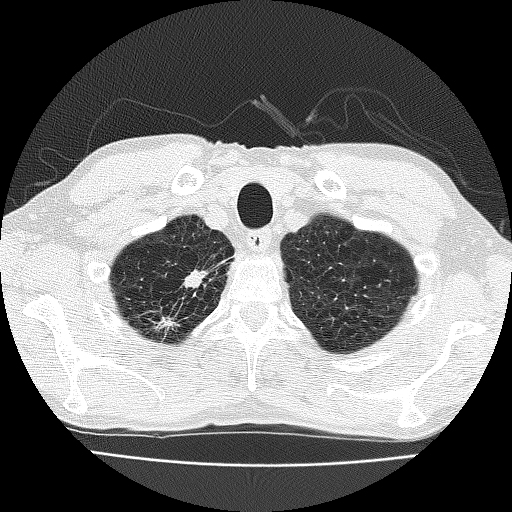
Chest CT (low-dose screening protocol), one axial image. Third screening round (two years after baseline). Lung window (W 1500 / L -600 HU). Lung (sharp) reconstruction kernel (FC51). Male, age 63 years at enrolment. Current smoker at enrolment.
Expert-annotated lung lesion, bounding box [x1, y1, x2, y2] px = [144, 257, 224, 336]. Reader record for this screening exam (exam-level; its link to the box is not recorded): non-calcified nodule or mass ≥4 mm, right upper lobe, 17 × 10 mm, spiculated (stellate) margins, soft tissue attenuation, pre-existing on the prior screen: yes; interval growth: yes. Later outcome: lung cancer diagnosed 28 days after this screen — adenocarcinoma, NOS, right upper lobe, moderately differentiated (G2), stage IIIB (AJCC 6th edition), 17 mm at pathology.